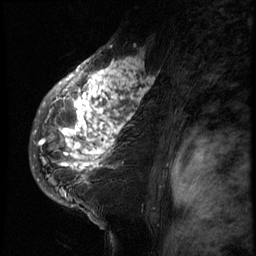
Breast MRI (dynamic contrast-enhanced), one sagittal slice. Slice 48 of 66 in the series (ordered by position). 3 images stored at this slice position (order not interpretable as contrast timing). 1.5 T. TE 4.2 ms, TR 8.9 ms. 2.5 mm slice thickness. 256 × 256 image matrix, field of view 200 × 200 mm. Patient: female, 39 years. Case-level facts recorded for this patient, not image findings: setting: breast cancer imaged before/during neoadjuvant chemotherapy; receptor status: HER2-positive.
Structures marked on this image (semi-automatic segmentation, software-assisted and operator-edited):
- analysis volume of interest (the breast-tissue region the enhancement analysis was run in; not a lesion): bounding box (x1, y1, x2, y2) in pixels: (29, 44, 166, 196)
- tumour enhancement mask (voxels above the 140 % enhancement threshold inside the analysis volume of interest): (38, 45, 154, 171)